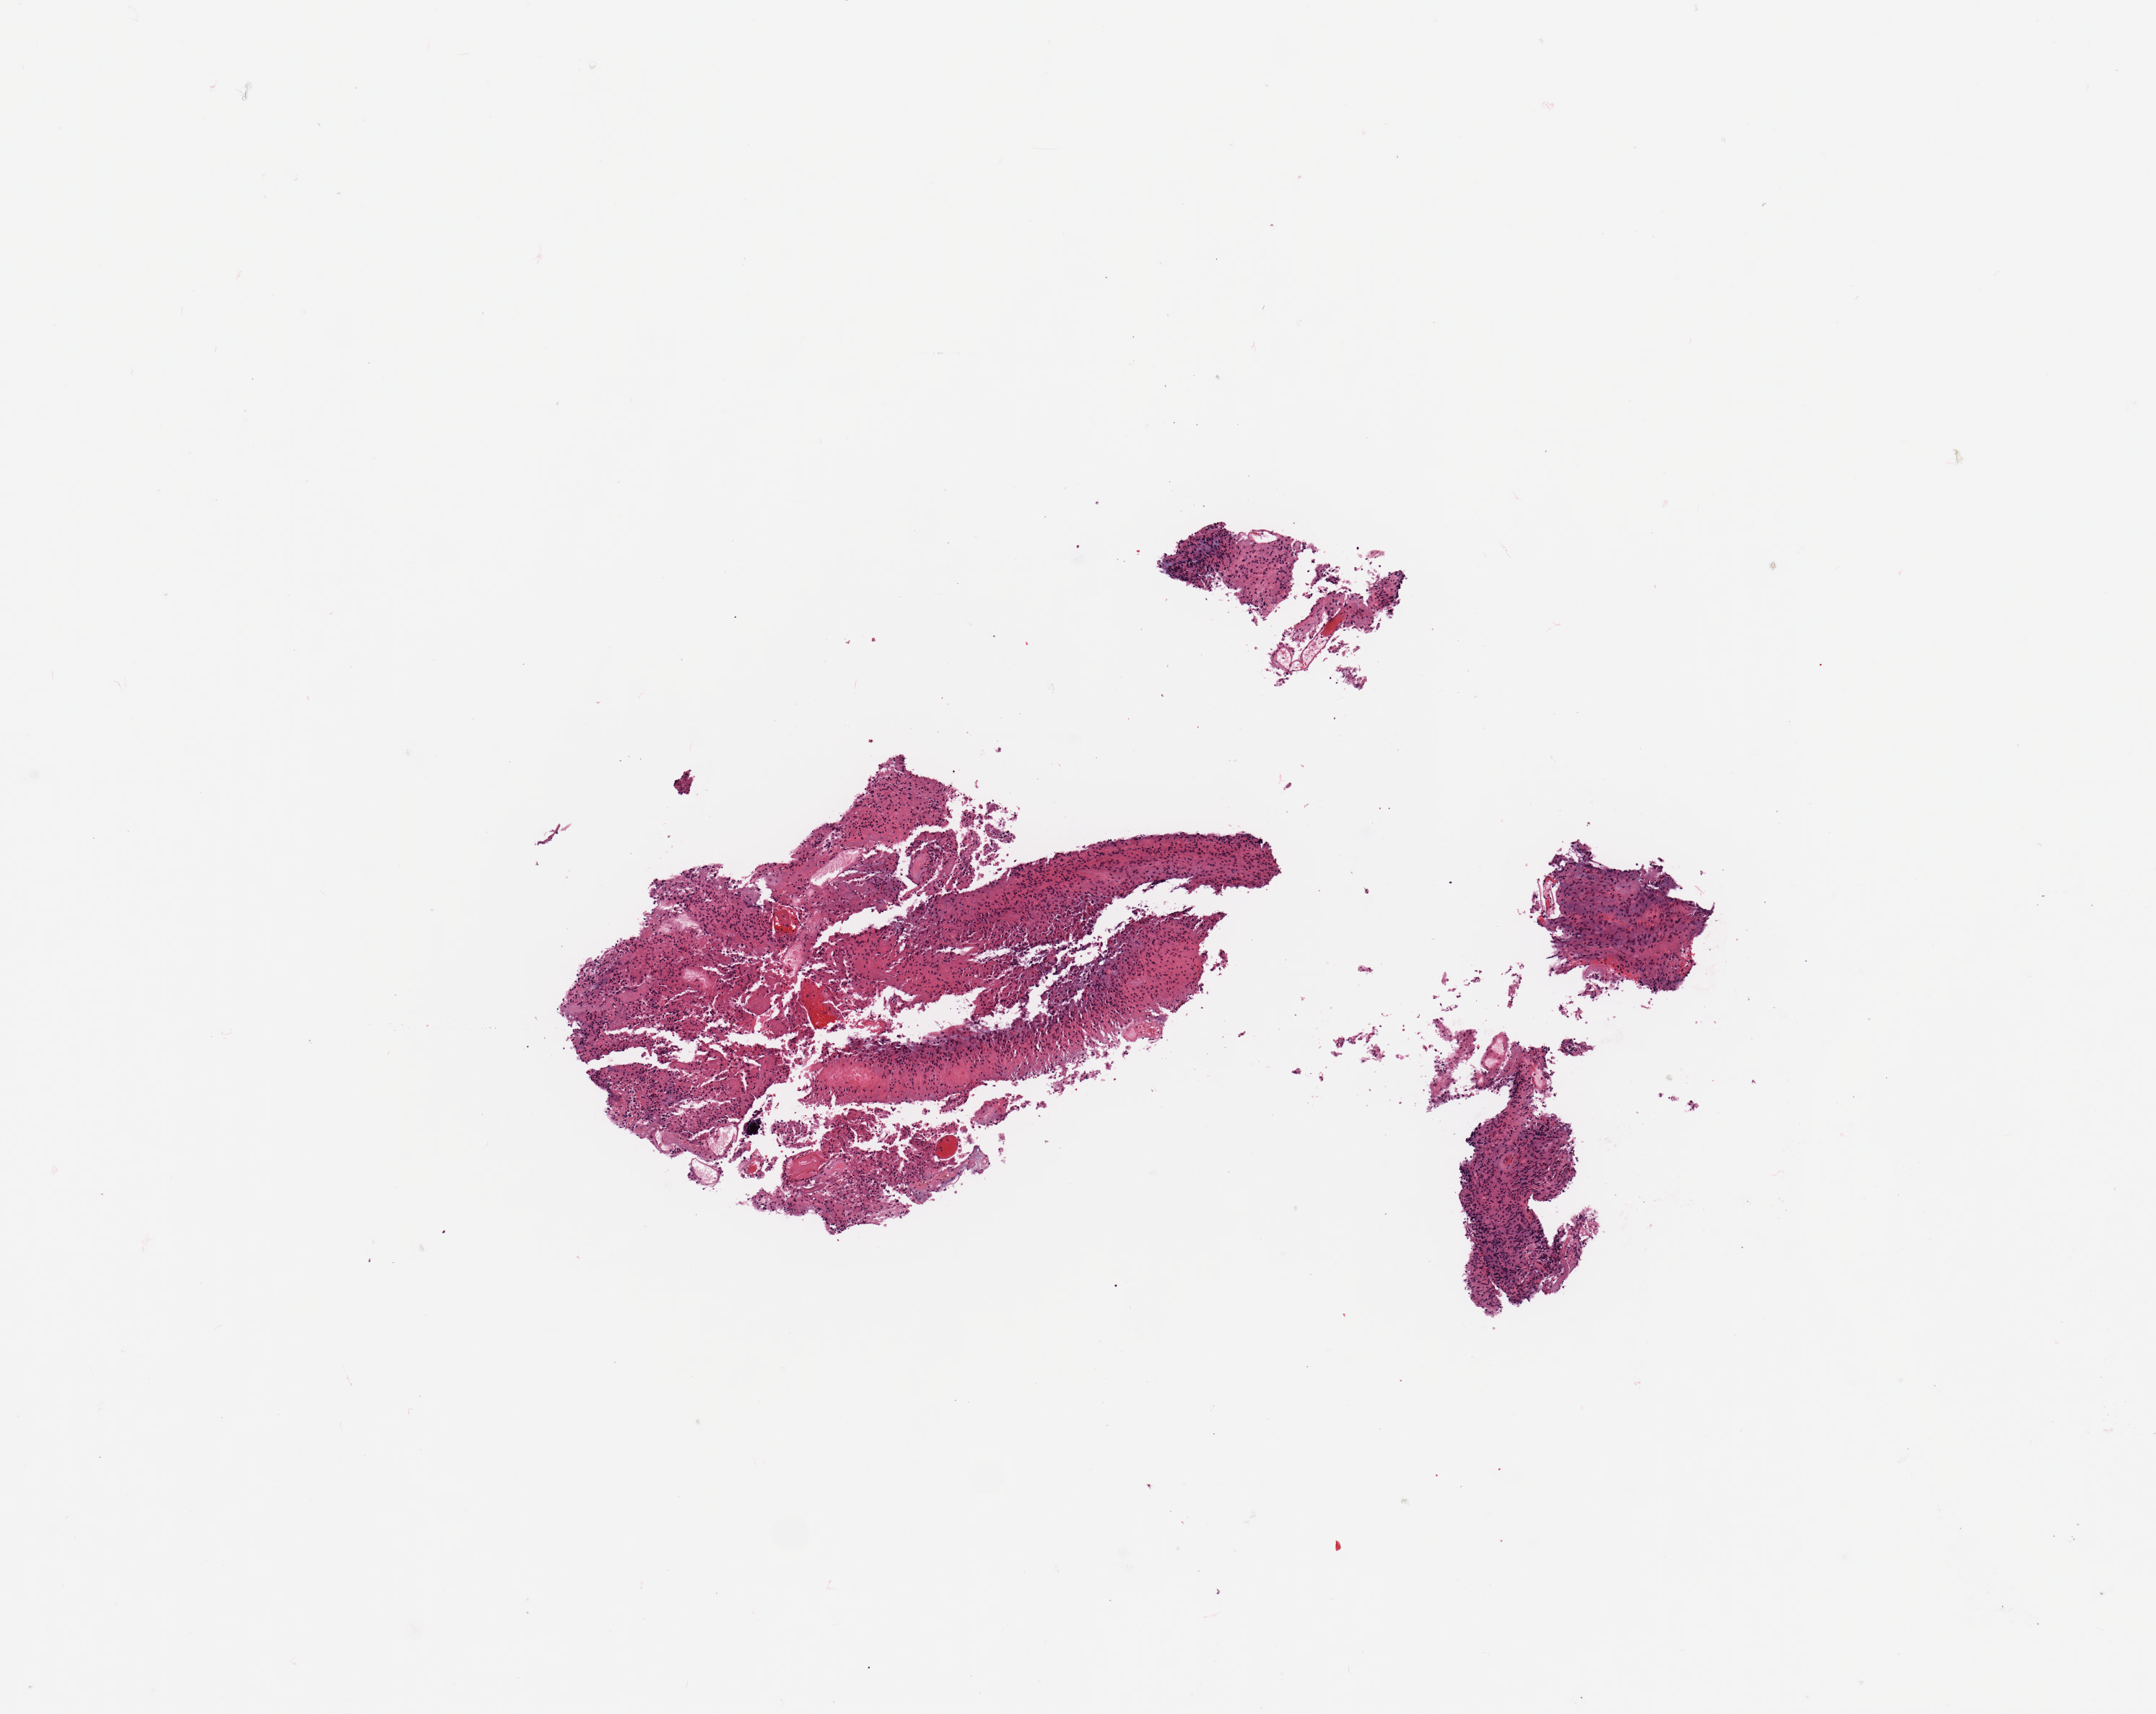
Whole-slide histology image, H&E-stained — low-resolution overview of the scanned area, about 5.9 x 4.7 mm (from a 20x scan); brain, tumour tissue. Male, 71 y/o.
Histologic diagnosis: Glioblastoma. Primary tumour site (as recorded): occipital lobe.